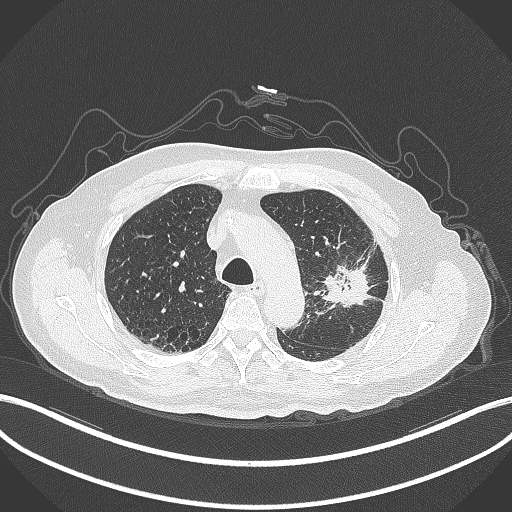
Chest CT, one axial slice; slice 218 of 331 in the series (ordered by position); lung window (W 1500 / L -600 HU); 1 mm slice thickness; 512 × 512 image matrix. Patient: male, 79 years. From the clinical record (not read from this slice): clinical TNM (as recorded): T2a N1 M1.
Structures marked on this image (bounding box drawn by a radiologist):
- lung tumour (recorded histology: adenocarcinoma): bounding box <319,245,383,307> (left, top, right, bottom; pixels)